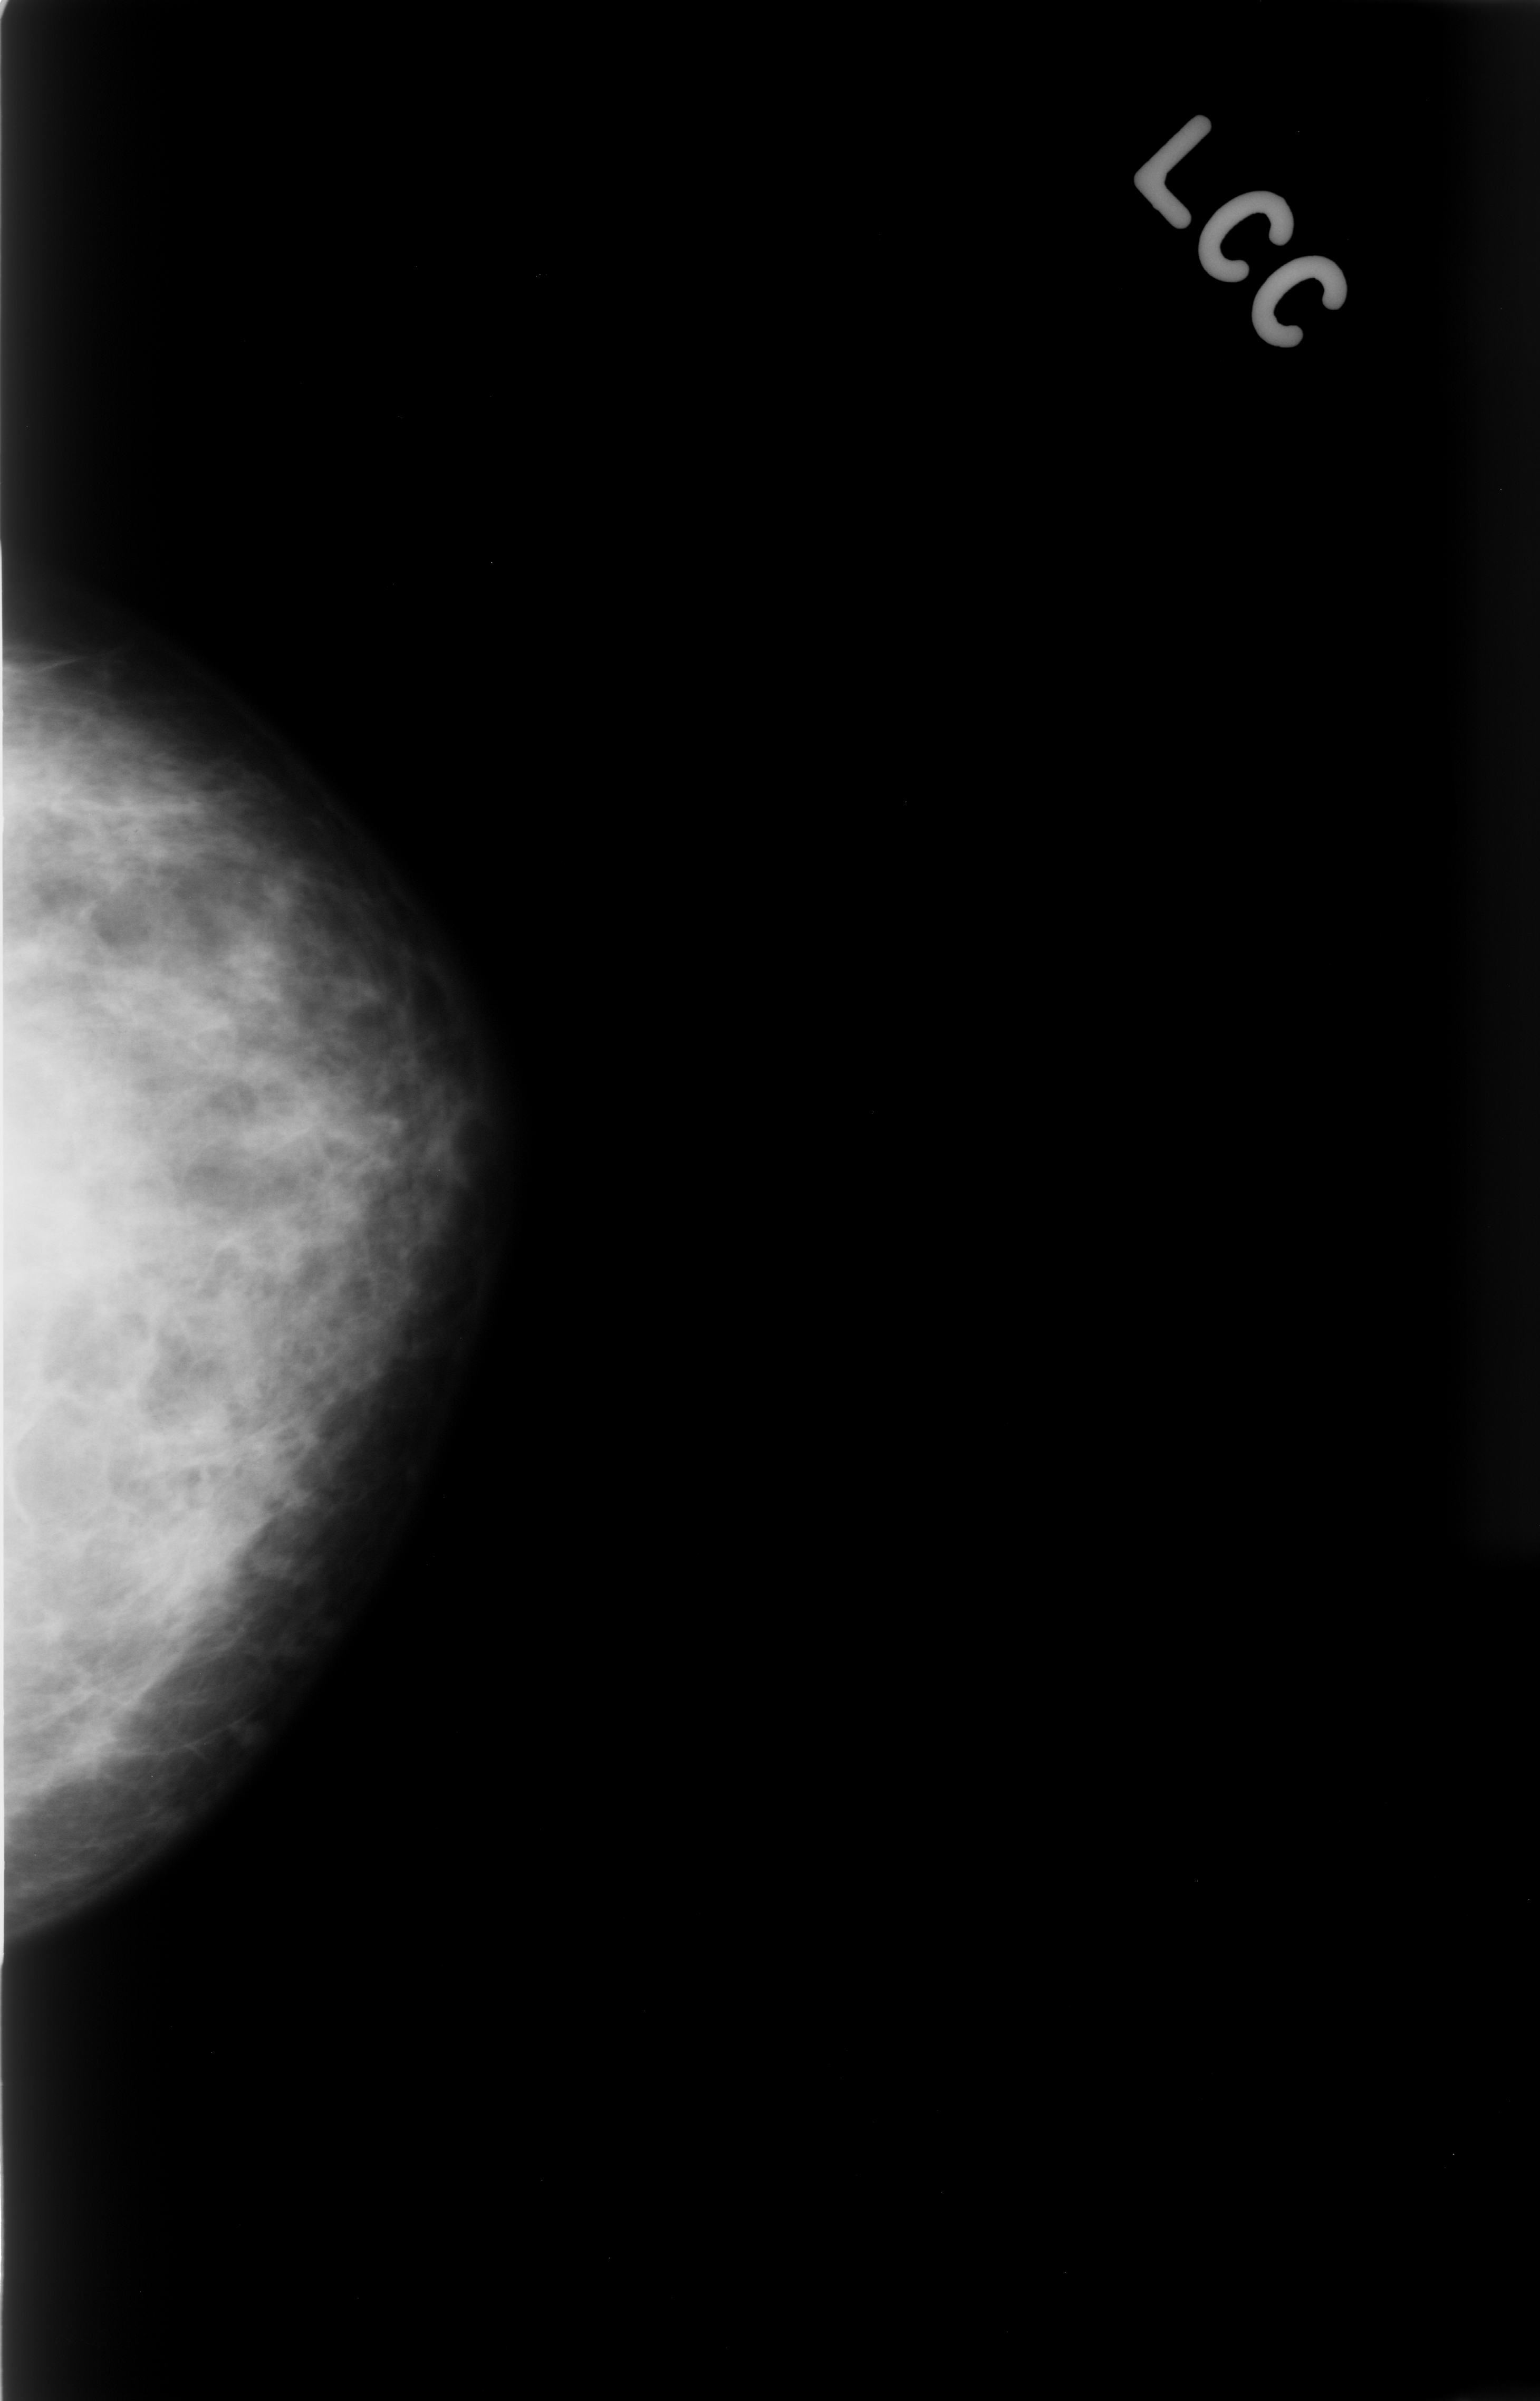
Digitized screen-film mammogram, left breast, craniocaudal (CC) view, BI-RADS breast density category 3 (scale 1–4).
- Radiologist-marked abnormalities on this image: mass, shape asymmetric breast tissue, margins ill defined; BI-RADS assessment category 5; subtlety rating 2 on a 1 (subtle) to 5 (obvious) scale; pathology (as recorded): malignant.